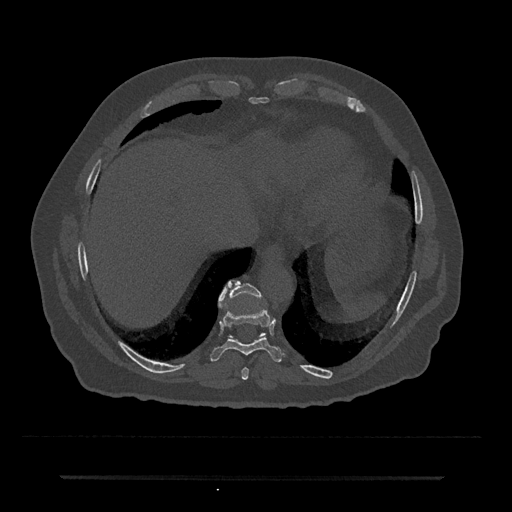
CT including the spine, one axial slice; position 272 of 797 along the scan axis; 120 kVp; bone window (W 1800 / L 400 HU); 0.5 mm slice thickness; 512 × 512 image matrix. Patient: male, 69 years. Case-level facts recorded for this patient, not image findings: primary cancer: prostate.
Annotated regions visible in this slice (semi-automatic segmentation, software-assisted and operator-edited):
- T10 vertebra: bounding box [x1, y1, x2, y2] px = [219, 280, 265, 336]
- T8 vertebra: [241, 367, 249, 380]
- T9 vertebra: [210, 288, 285, 362]